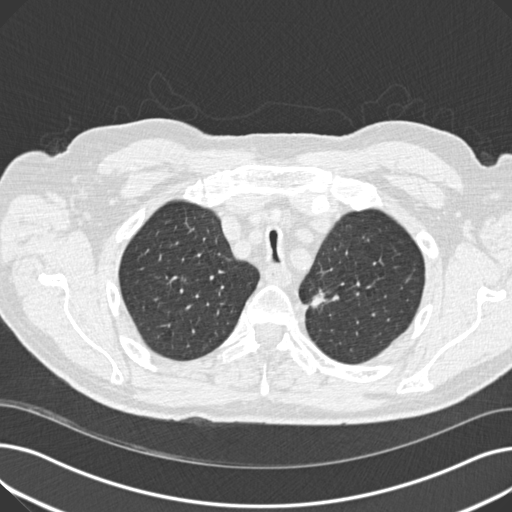
Low-dose screening chest CT, one axial slice. Reconstruction kernel B30f. Lung window (W 1500 / L -600 HU). 2 mm slice thickness. 512 × 512 image matrix, field of view 370 × 370 mm.
Structures marked on this image (outlined manually by an expert reader):
- lesion 1 (tumor, upper lobe of left lung): bounding box [x1, y1, x2, y2] px = [310, 290, 326, 307]